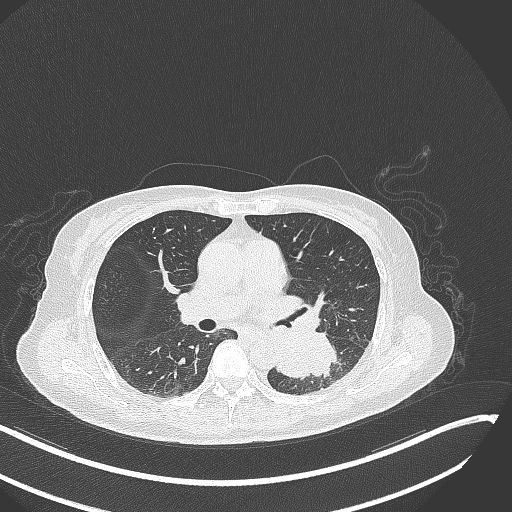
Chest CT, one axial slice. Slice 155 of 342 in the series (ordered by position). Reconstruction kernel B70f. Lung window (W 1500 / L -600 HU). 1 mm slice thickness. 512 × 512 image matrix, field of view 400 × 400 mm. Female patient, age 64 years. Case-level facts recorded for this patient, not image findings: clinical TNM (as recorded): T3 N1 M1; histopathological grade: G3.
Annotated regions visible in this slice (bounding box drawn by a radiologist):
- lung tumour (recorded histology: small cell carcinoma): bounding box [x1, y1, x2, y2] px = [273, 327, 342, 382]